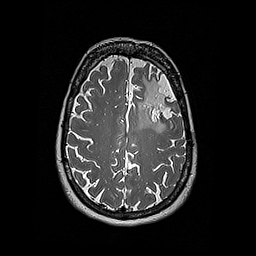
Brain MRI from a brain-tumour surgery series, one axial slice. 256 × 256 image matrix. Case-level facts recorded for this patient, not image findings: histopathology: Oligodendroglioma; WHO grade: 2; IDH mutation: yes; tumour location: Left Frontal.
Outlined on this slice (outlined manually by an expert reader):
- tumour: bounding box <134,78,157,129> (left, top, right, bottom; pixels)